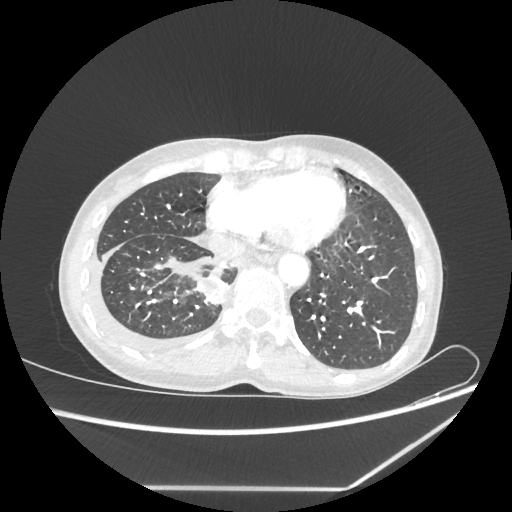
Chest CT, one axial slice. Position 64 of 237 along the scan axis. Lung window (W 1500 / L -600 HU). 1.25 mm slice thickness. 512 × 512 image matrix, field of view 364 × 364 mm. Patient: female, 59 years. Case-level facts recorded for this patient, not image findings: clinical TNM (as recorded): T1c N1 M1.
Outlined on this slice (rectangle marked by the reading radiologist):
- lung tumour (recorded histology: adenocarcinoma): bounding box (x1, y1, x2, y2) in pixels: (192, 274, 229, 304)